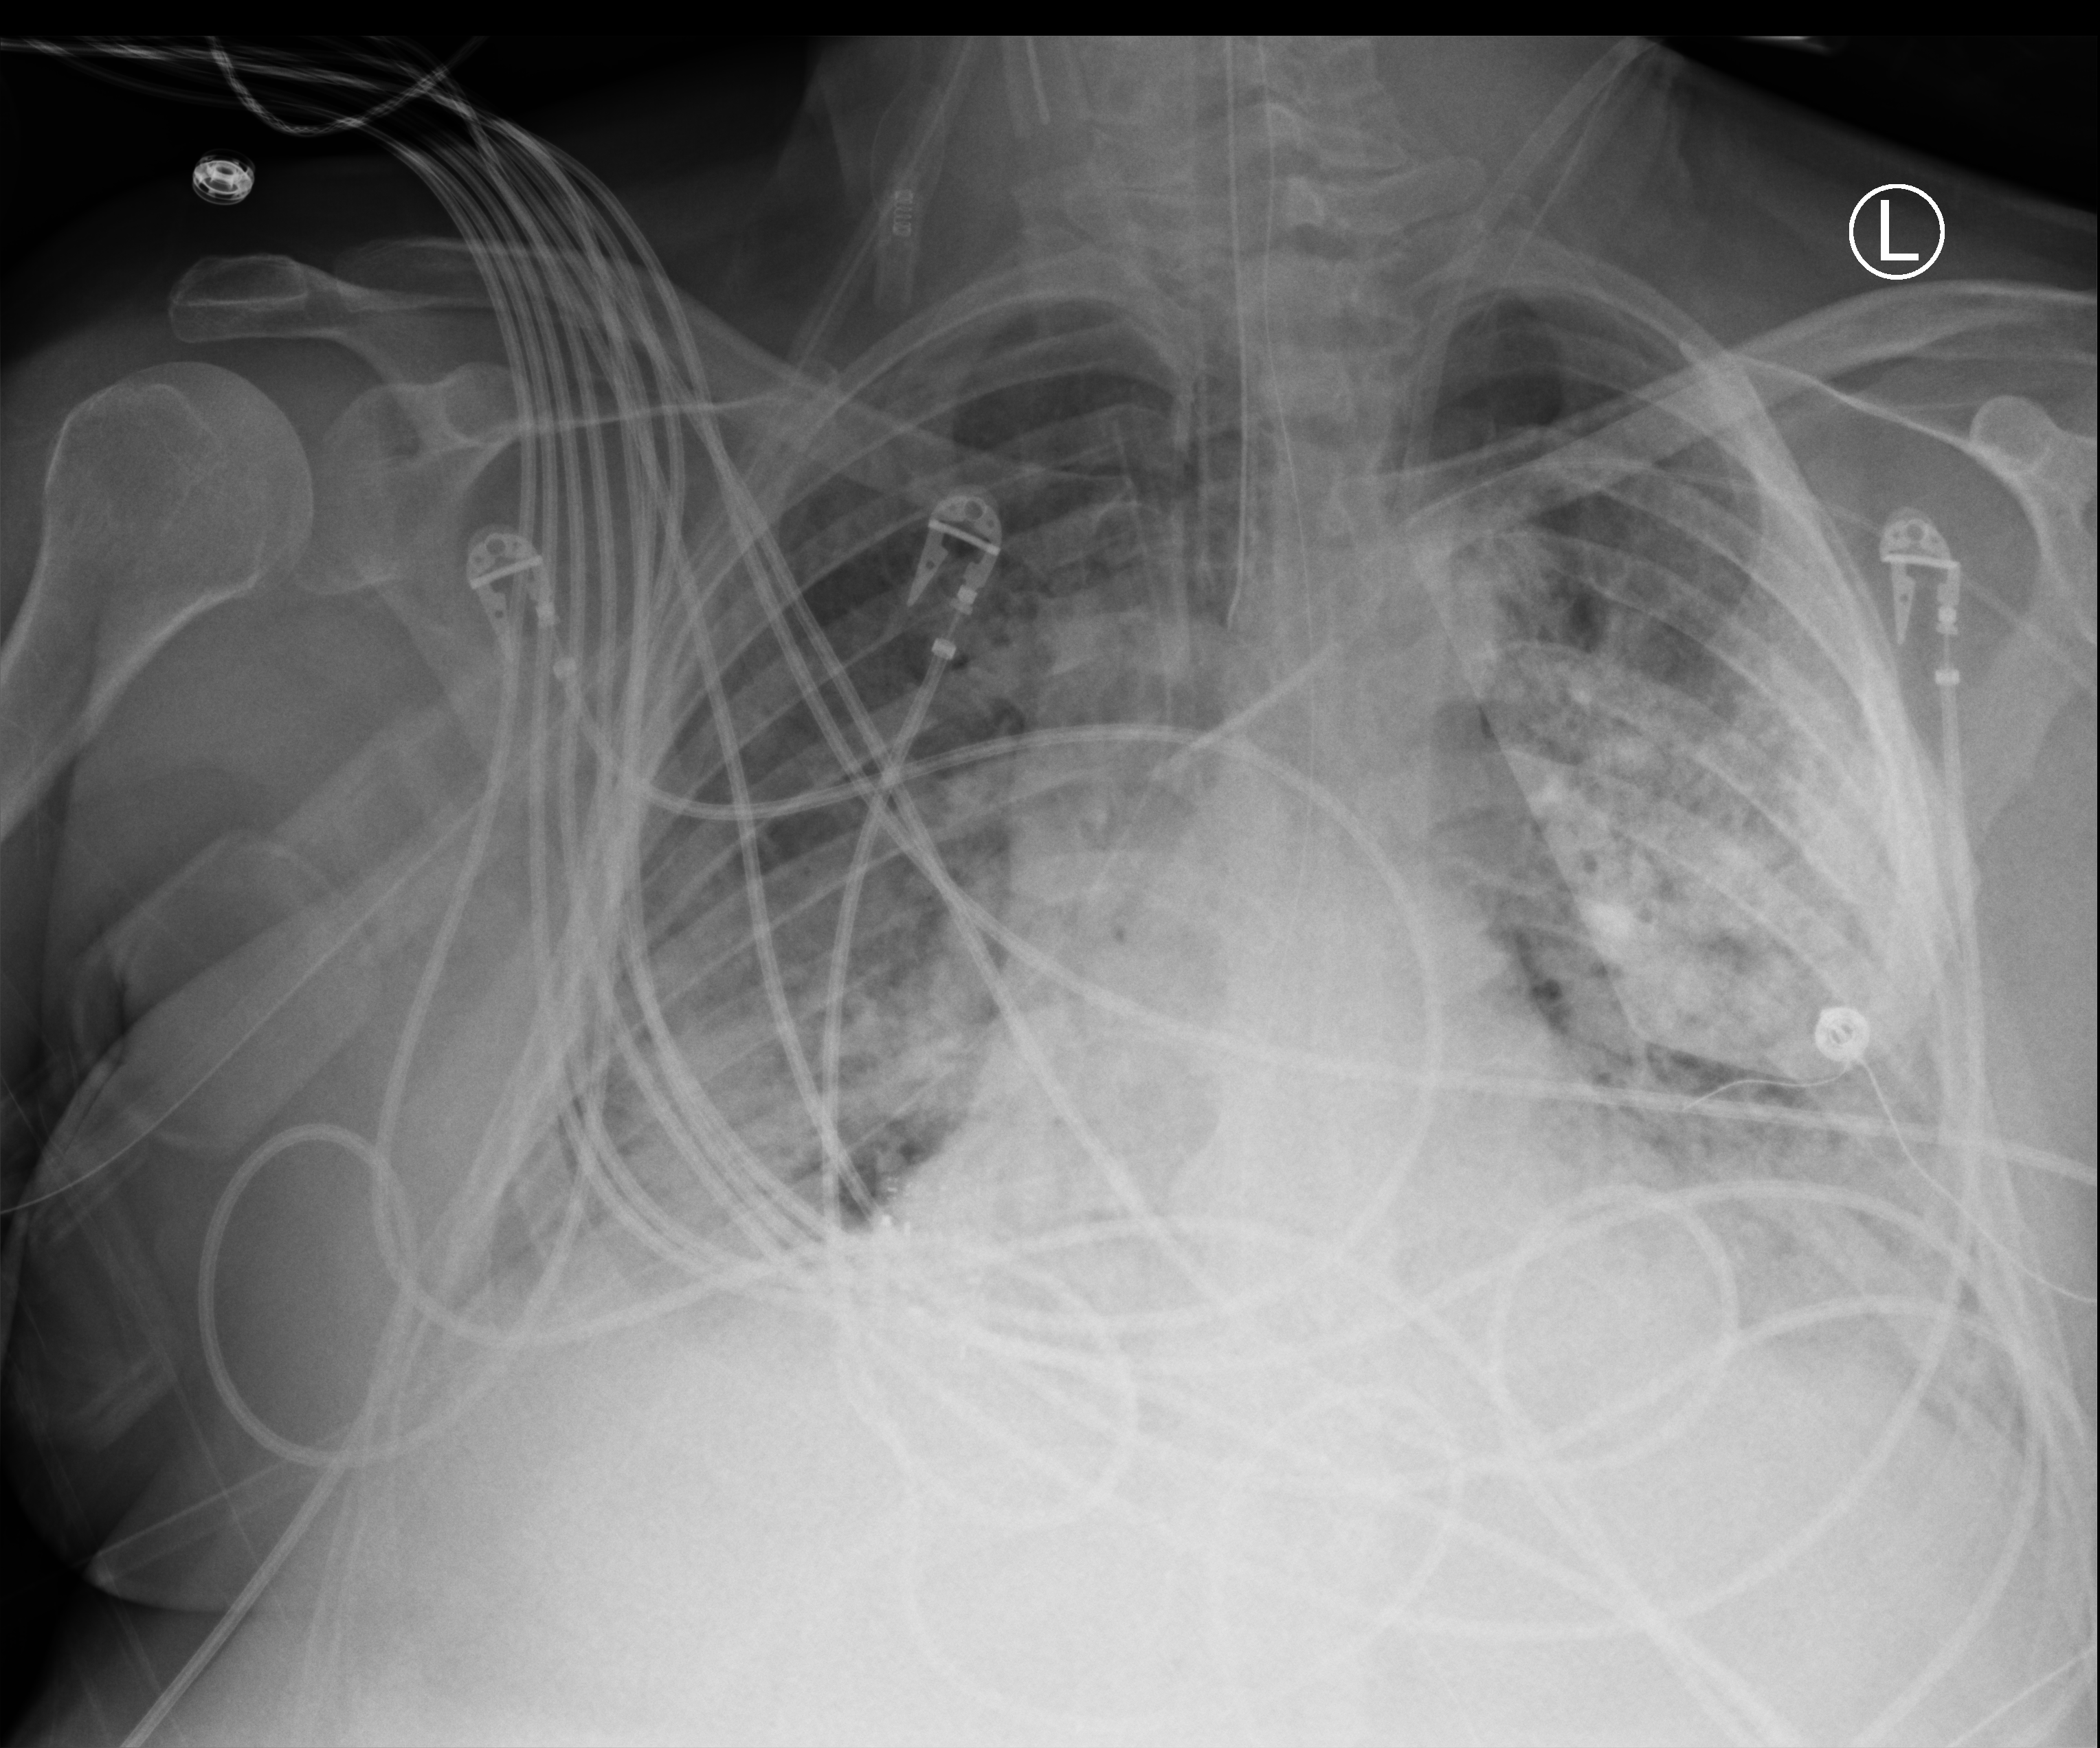
Bedside chest radiograph (computed radiography), anteroposterior (AP) projection. Patient hospitalised with COVID-19; male, aged 18–59 years.
Admission-level facts for this patient (not findings on this image; timing relative to this image not recorded):
- mechanically ventilated during this hospital stay: yes